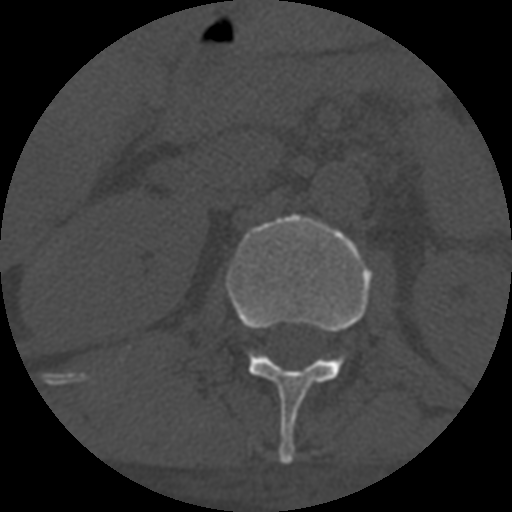
CT including the spine, one axial slice; slice 283 of 708 in the series (ordered by position); reconstruction kernel STANDARD; 120 kVp; one of 3 acquisitions stored at this slice position; bone window (W 1800 / L 400 HU); 512 × 512 image matrix, field of view 160 × 160 mm. Patient age 55 years. Case-level facts recorded for this patient, not image findings: primary cancer: colon; vertebrae with lytic lesions (as recorded): T12, L1, L5.
Outlined on this slice (semi-automatic segmentation, software-assisted and operator-edited):
- L1 vertebra: bounding box <226,215,372,464> (left, top, right, bottom; pixels)